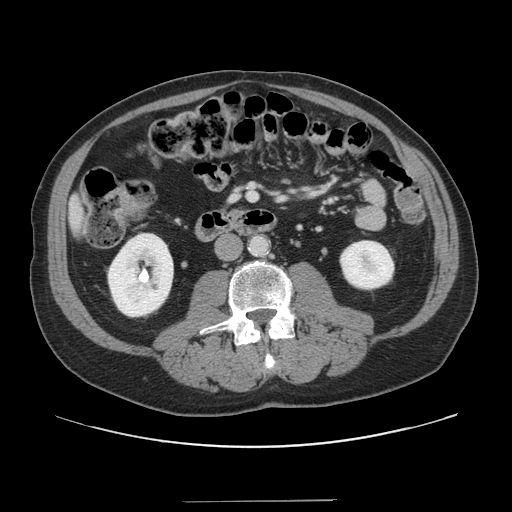
Contrast-enhanced abdominal CT, one axial slice. Position 35 of 151 along the scan axis. 120 kVp. Intravenous contrast given. Soft-tissue window (W 400 / L 40 HU). 2.5 mm slice thickness. 512 × 512 image matrix. Male patient, age 63 years. From the clinical record (not read from this slice): diagnosis: colorectal cancer liver metastases, imaged before liver resection; multiple liver metastases: no; largest metastasis: 2.1 cm; disease in both lobes: no.
Structures marked on this image (expert manual segmentation):
- liver: bounding box [x1, y1, x2, y2] px = [71, 199, 83, 234]
- planned liver remnant (the part of the liver to remain after resection): [70, 198, 84, 234]
- portal vein (with intrahepatic branches): [249, 193, 257, 200]